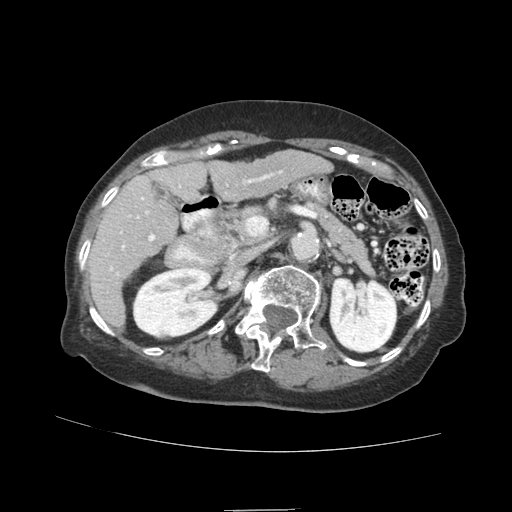
Contrast-enhanced abdominal CT (liver protocol), one axial slice. Position 43 of 89 along the scan axis. Soft-tissue window (W 400 / L 40 HU). 2.5 mm slice thickness. 512 × 512 image matrix, field of view 360 × 360 mm. Case-level facts recorded for this patient, not image findings: diagnosis: hepatocellular carcinoma (patient treated with transarterial chemoembolisation; whether this scan precedes or follows treatment is not stated here); TNM stage (as recorded): Stage-II; Child-Pugh class: A.
Structures marked on this image (semi-automatically segmented with operator editing):
- liver parenchyma outside the tumour (the mass and vessels are separate outlines, so this box may not span the whole liver): box from (x=88, y=150) to (x=332, y=327) px
- liver vessels: (x=109, y=170)–(x=283, y=276)